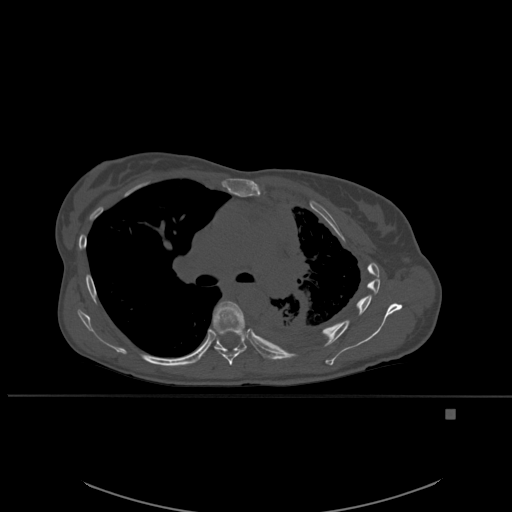
CT including the spine, one axial slice; slice 376 of 537 in the series (ordered by position); bone window (W 1800 / L 400 HU); 1.5 mm slice thickness; 512 × 512 image matrix. Patient: female, 45 years. Case-level facts recorded for this patient, not image findings: primary cancer: lung.
Annotated regions visible in this slice (semi-automatic segmentation, software-assisted and operator-edited):
- T6 vertebra: bounding box [x1, y1, x2, y2] px = [213, 301, 248, 366]
- T7 vertebra: [199, 315, 264, 360]